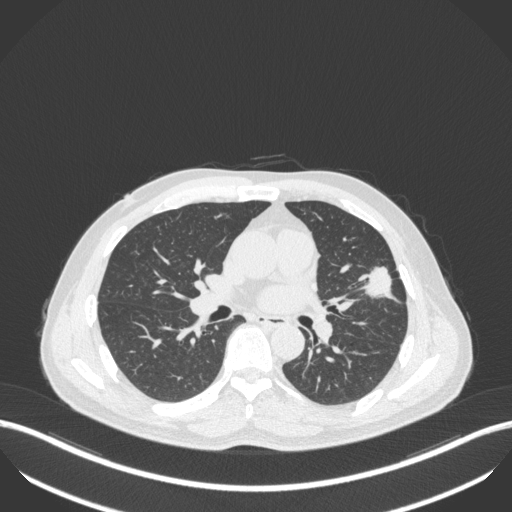
Chest CT, one axial slice. Position 216 of 418 along the scan axis. Lung window (W 1500 / L -600 HU). 1 mm slice thickness. 512 × 512 image matrix, field of view 400 × 400 mm. Male patient, age 55 years. From the clinical record (not read from this slice): clinical TNM (as recorded): T1c N0 M0; histopathological grade: G2-3.
Annotated regions visible in this slice (rectangle marked by the reading radiologist):
- lung tumour (recorded histology: adenocarcinoma): bounding box (x1, y1, x2, y2) in pixels: (354, 258, 400, 303)